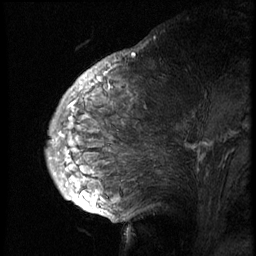
Breast MRI (dynamic contrast-enhanced), one sagittal slice; position 31 of 74 along the scan axis; 3 images stored at this slice position (order not interpretable as contrast timing); 1.5 T; TE 4.2 ms, TR 8.9 ms; 2.5 mm slice thickness; 256 × 256 image matrix. Patient: female, 57 years. Case-level facts recorded for this patient, not image findings: setting: breast cancer imaged before/during neoadjuvant chemotherapy; receptor status: HER2-positive.
Structures marked on this image (semi-automatic segmentation, software-assisted and operator-edited):
- analysis volume of interest (the breast-tissue region the enhancement analysis was run in; not a lesion): bounding box [x1, y1, x2, y2] px = [51, 67, 249, 173]
- tumour enhancement mask (voxels above the 140 % enhancement threshold inside the analysis volume of interest): [74, 85, 112, 104]